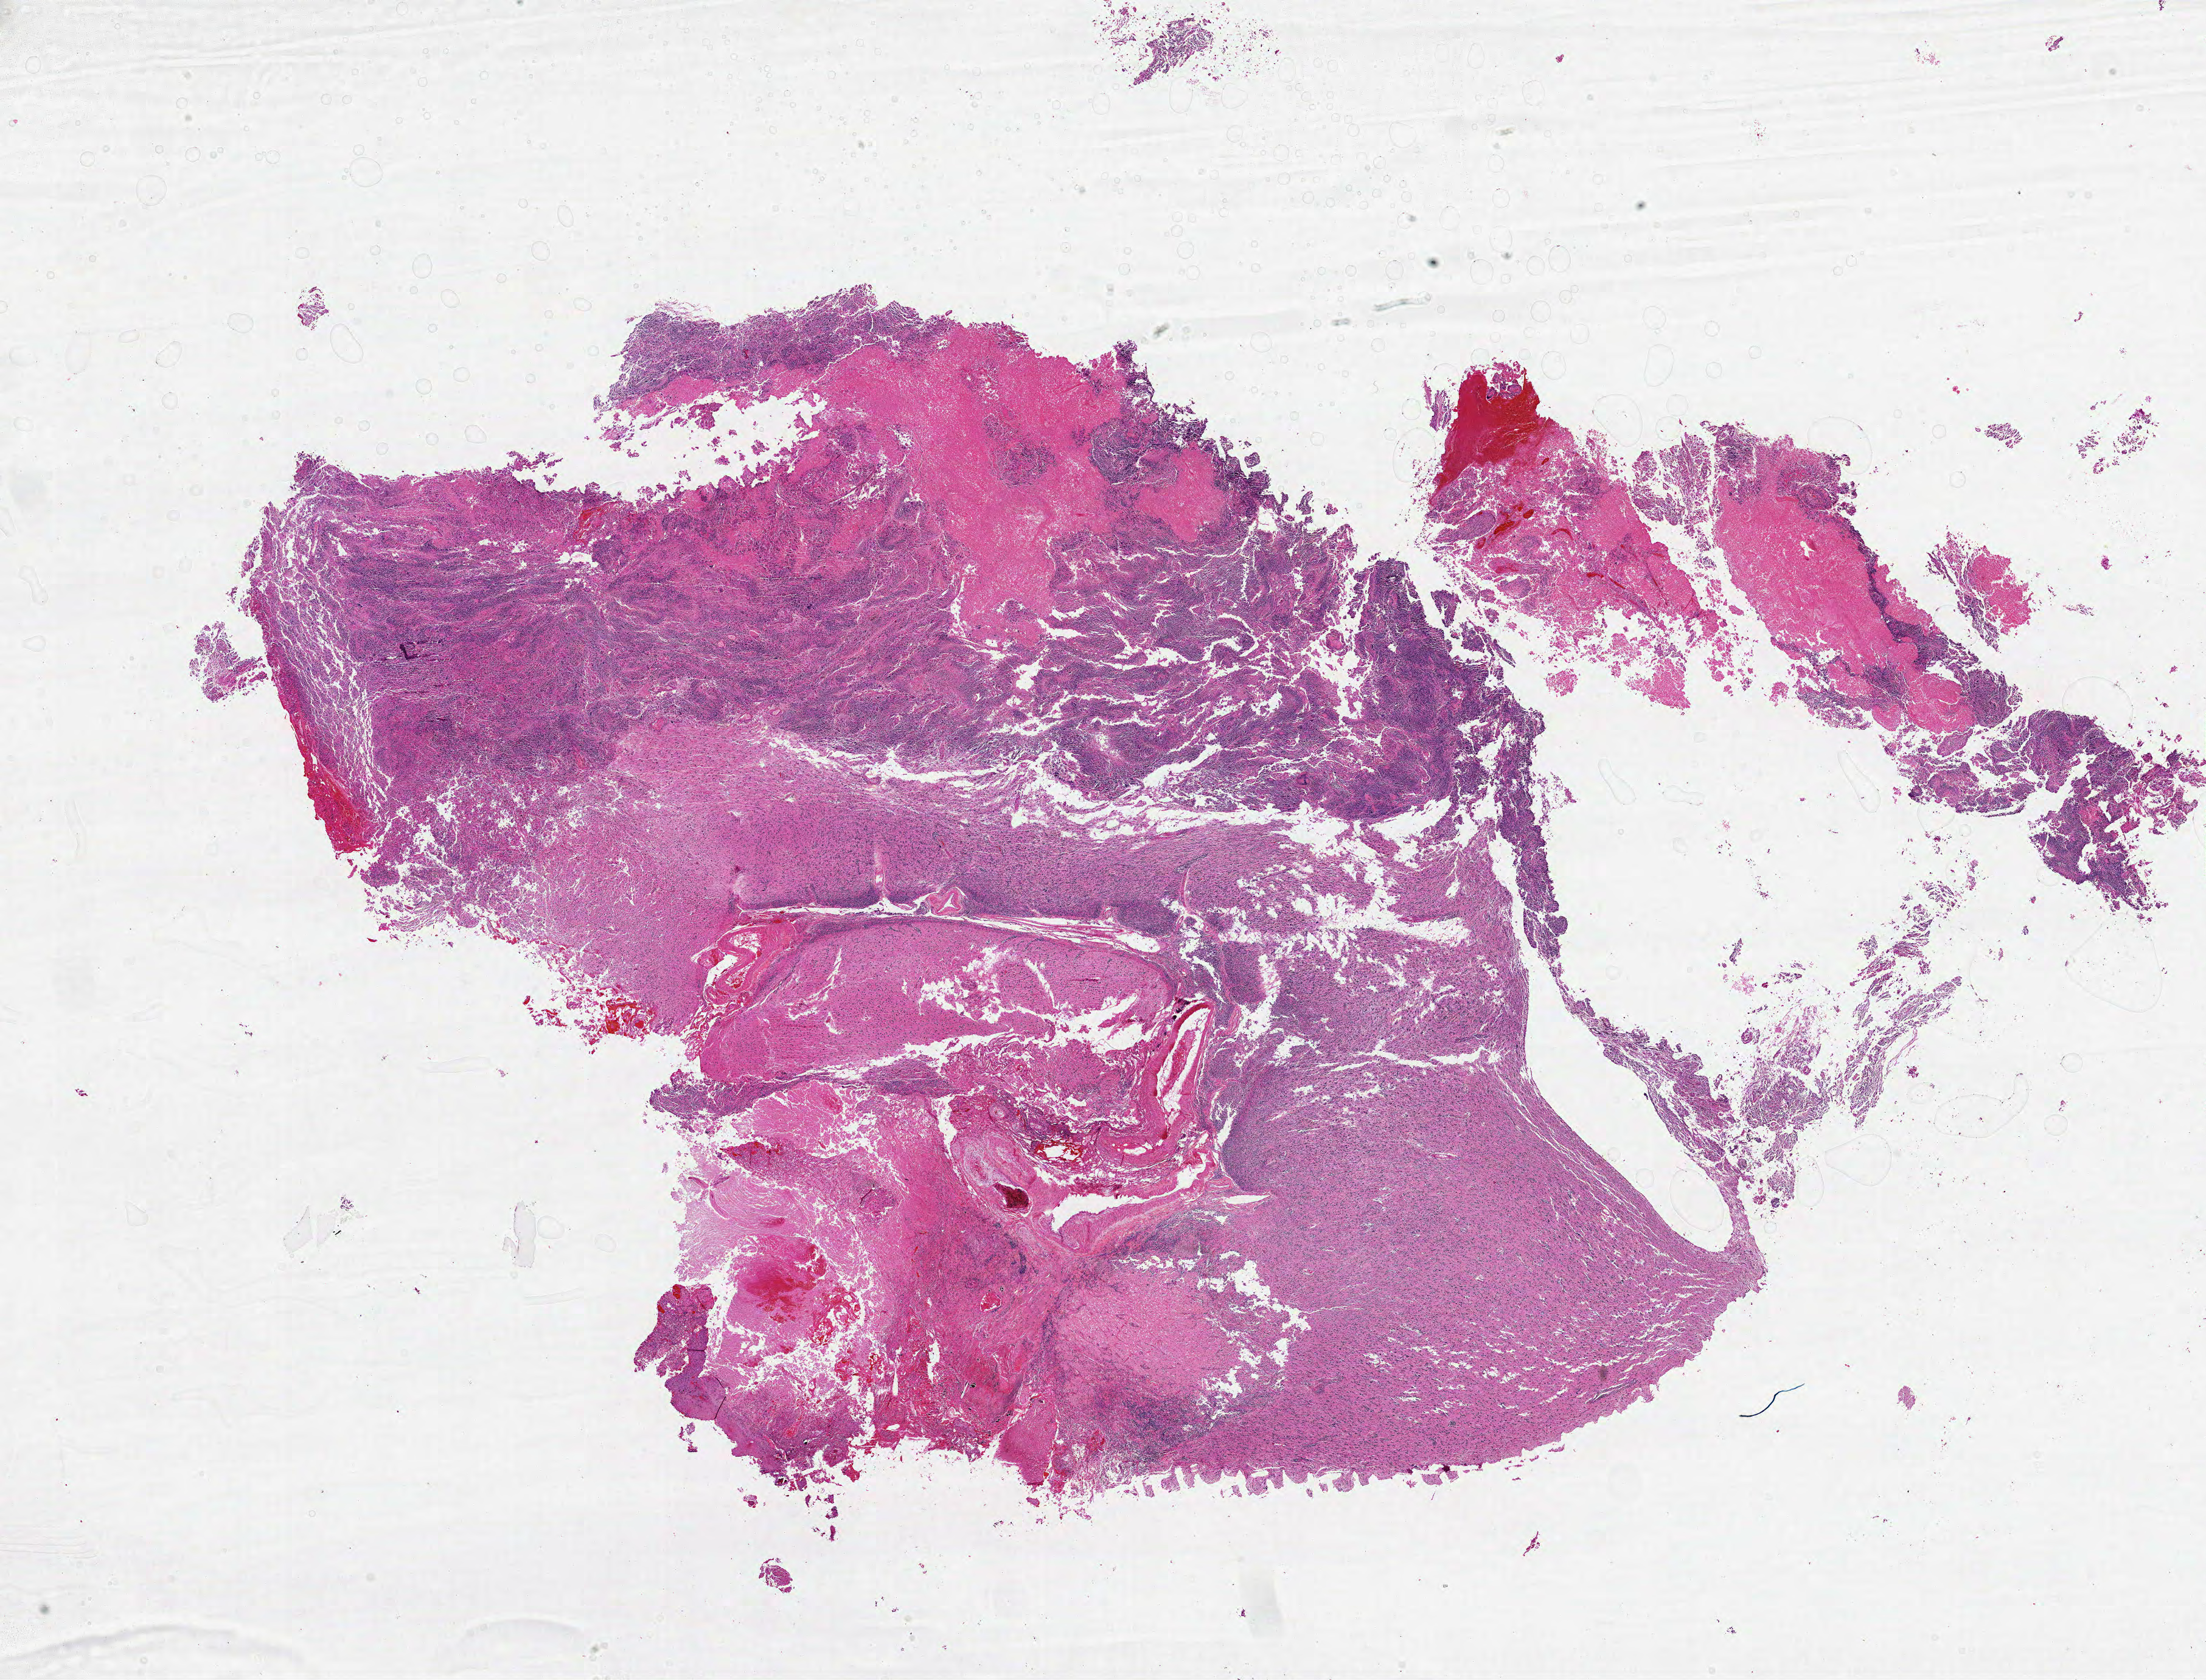
Digitized Hematoxylin and eosin (H&E) stained tissue section (whole slide) — low-resolution overview of the scanned area, about 29.0 x 22.1 mm (acquisition: 20x scan); formalin-fixed paraffin-embedded (FFPE) diagnostic section; brain, primary tumour sample. Male patient; age at initial diagnosis 24 years.
* histologic diagnosis: Glioblastoma